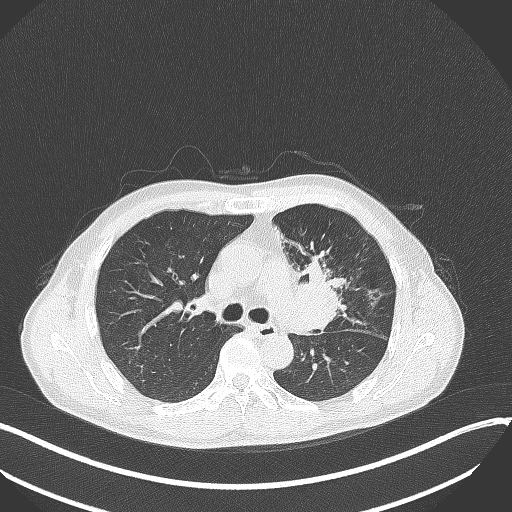
Chest CT, one axial slice; slice 215 of 411 in the series (ordered by position); lung window (W 1500 / L -600 HU); 512 × 512 image matrix, field of view 400 × 400 mm. Patient: male, 56 years. Case-level facts recorded for this patient, not image findings: clinical TNM (as recorded): T2a N0 M0.
Outlined on this slice (rectangle marked by the reading radiologist):
- lung tumour (recorded histology: squamous cell carcinoma): box from (x=290, y=251) to (x=344, y=337) px